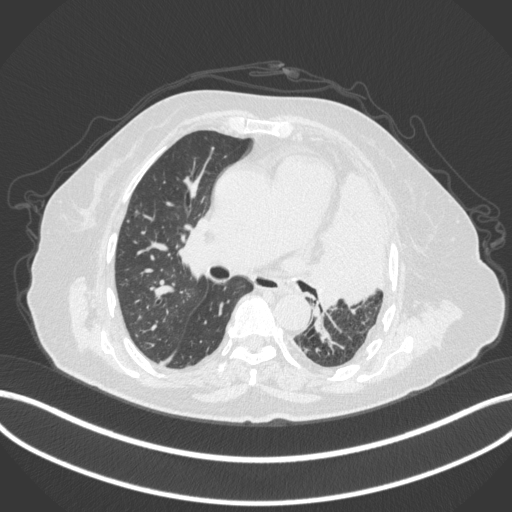
Chest CT, one axial slice. Slice 217 of 399 in the series (ordered by position). Reconstruction kernel B31f. 120 kVp. Lung window (W 1500 / L -600 HU). 1 mm slice thickness. 512 × 512 image matrix, field of view 400 × 400 mm. Patient: female, 75 years. From the clinical record (not read from this slice): clinical TNM (as recorded): T3 N3 M1.
Structures marked on this image (bounding box drawn by a radiologist):
- lung tumour (recorded histology: adenocarcinoma): bounding box [x1, y1, x2, y2] px = [313, 173, 394, 310]